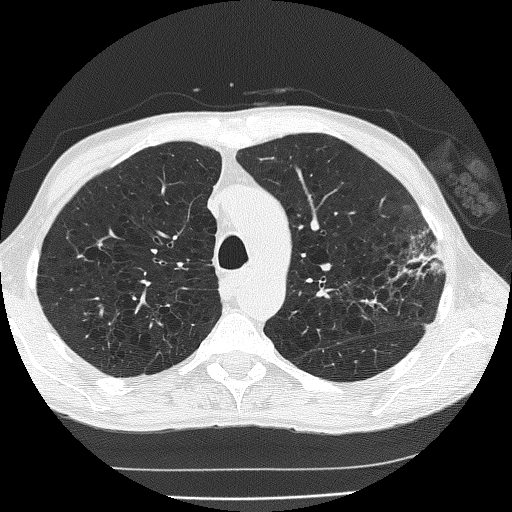
Axial slice from a low-dose chest CT screening exam. Second annual screen. Lung window (W 1500 / L -600 HU). 120 kVp. Male, age 60 years at enrolment.
- Expert reader's lesion annotation, box from (x=346, y=229) to (x=450, y=335) px.
- The screening reader recorded 2 non-calcified nodules or masses ≥4 mm on this exam (left upper lobe, left upper lobe); which of them this box marks is not recorded.
- Official screen result: positive, other.